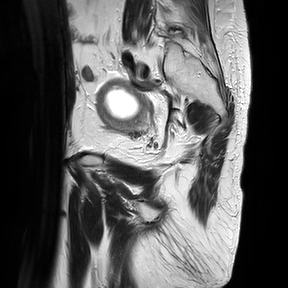
Pelvic MRI for cervical cancer, one sagittal slice; T2-weighted; 1.5 T; TE 100 ms, TR 4816.3 ms; 288 × 288 image matrix. Patient: female, 74 years.
Outlined on this slice (outlined manually by an expert reader):
- uterus and cervix: bounding box <96,77,151,134> (left, top, right, bottom; pixels)